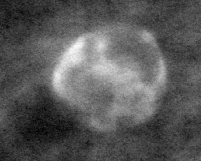
Crop from a digitized film mammogram around one marked abnormality; right breast; MLO view; BI-RADS breast density category 1 (scale 1–4).
Calcifications, morphology eggshell; BI-RADS assessment category 2; benign without callback (not worked up further).